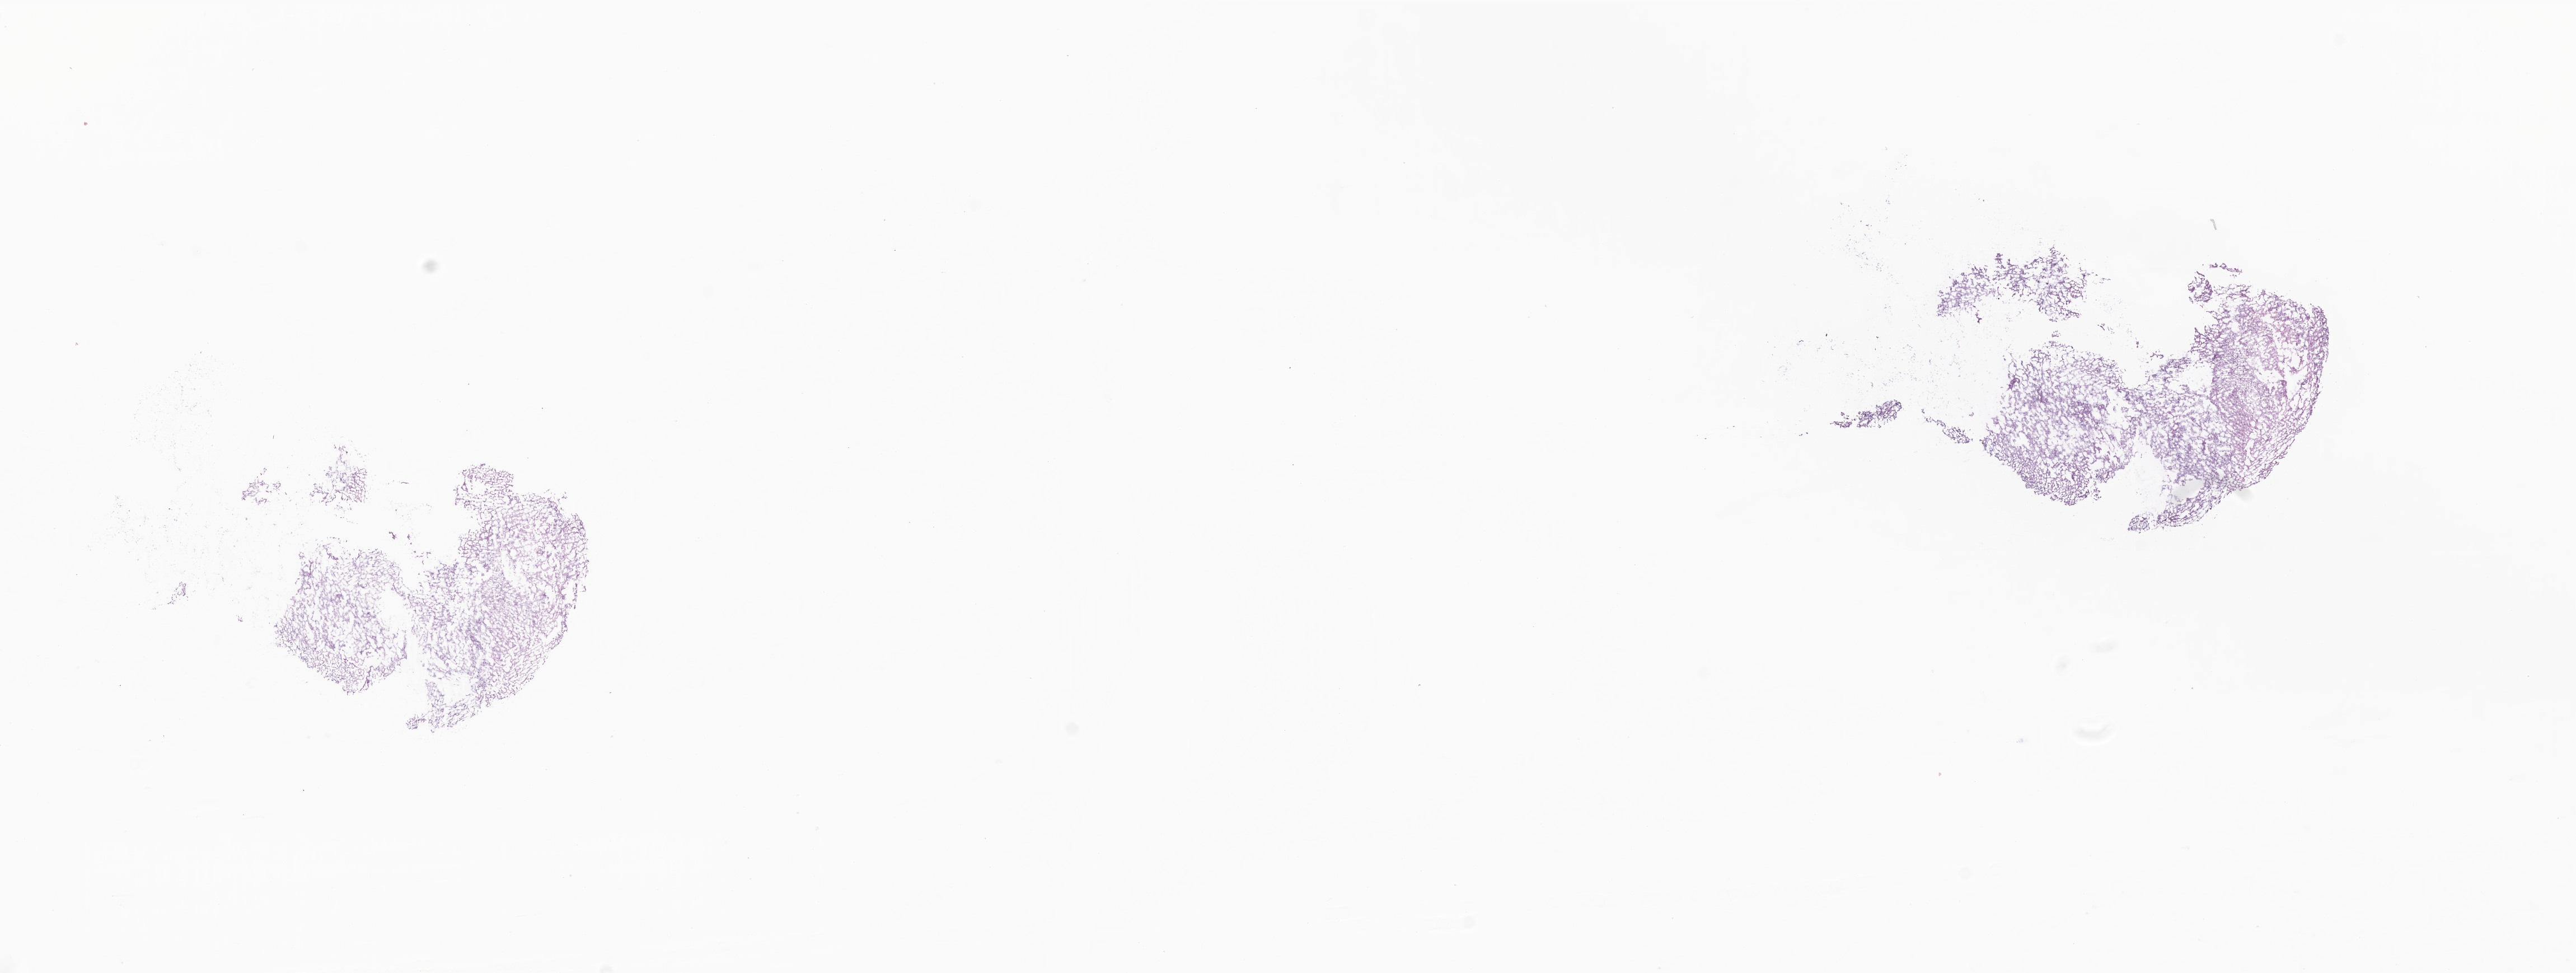
H&E whole-slide image of tumor tissue from the brain — shown as a low-resolution overview of the whole scanned area (about 19.4 x 7.3 mm). Frozen section. Female patient, age 274 days.
• diagnosis (ICD-O-3 morphology term): Neoplasm, uncertain whether benign or malignant